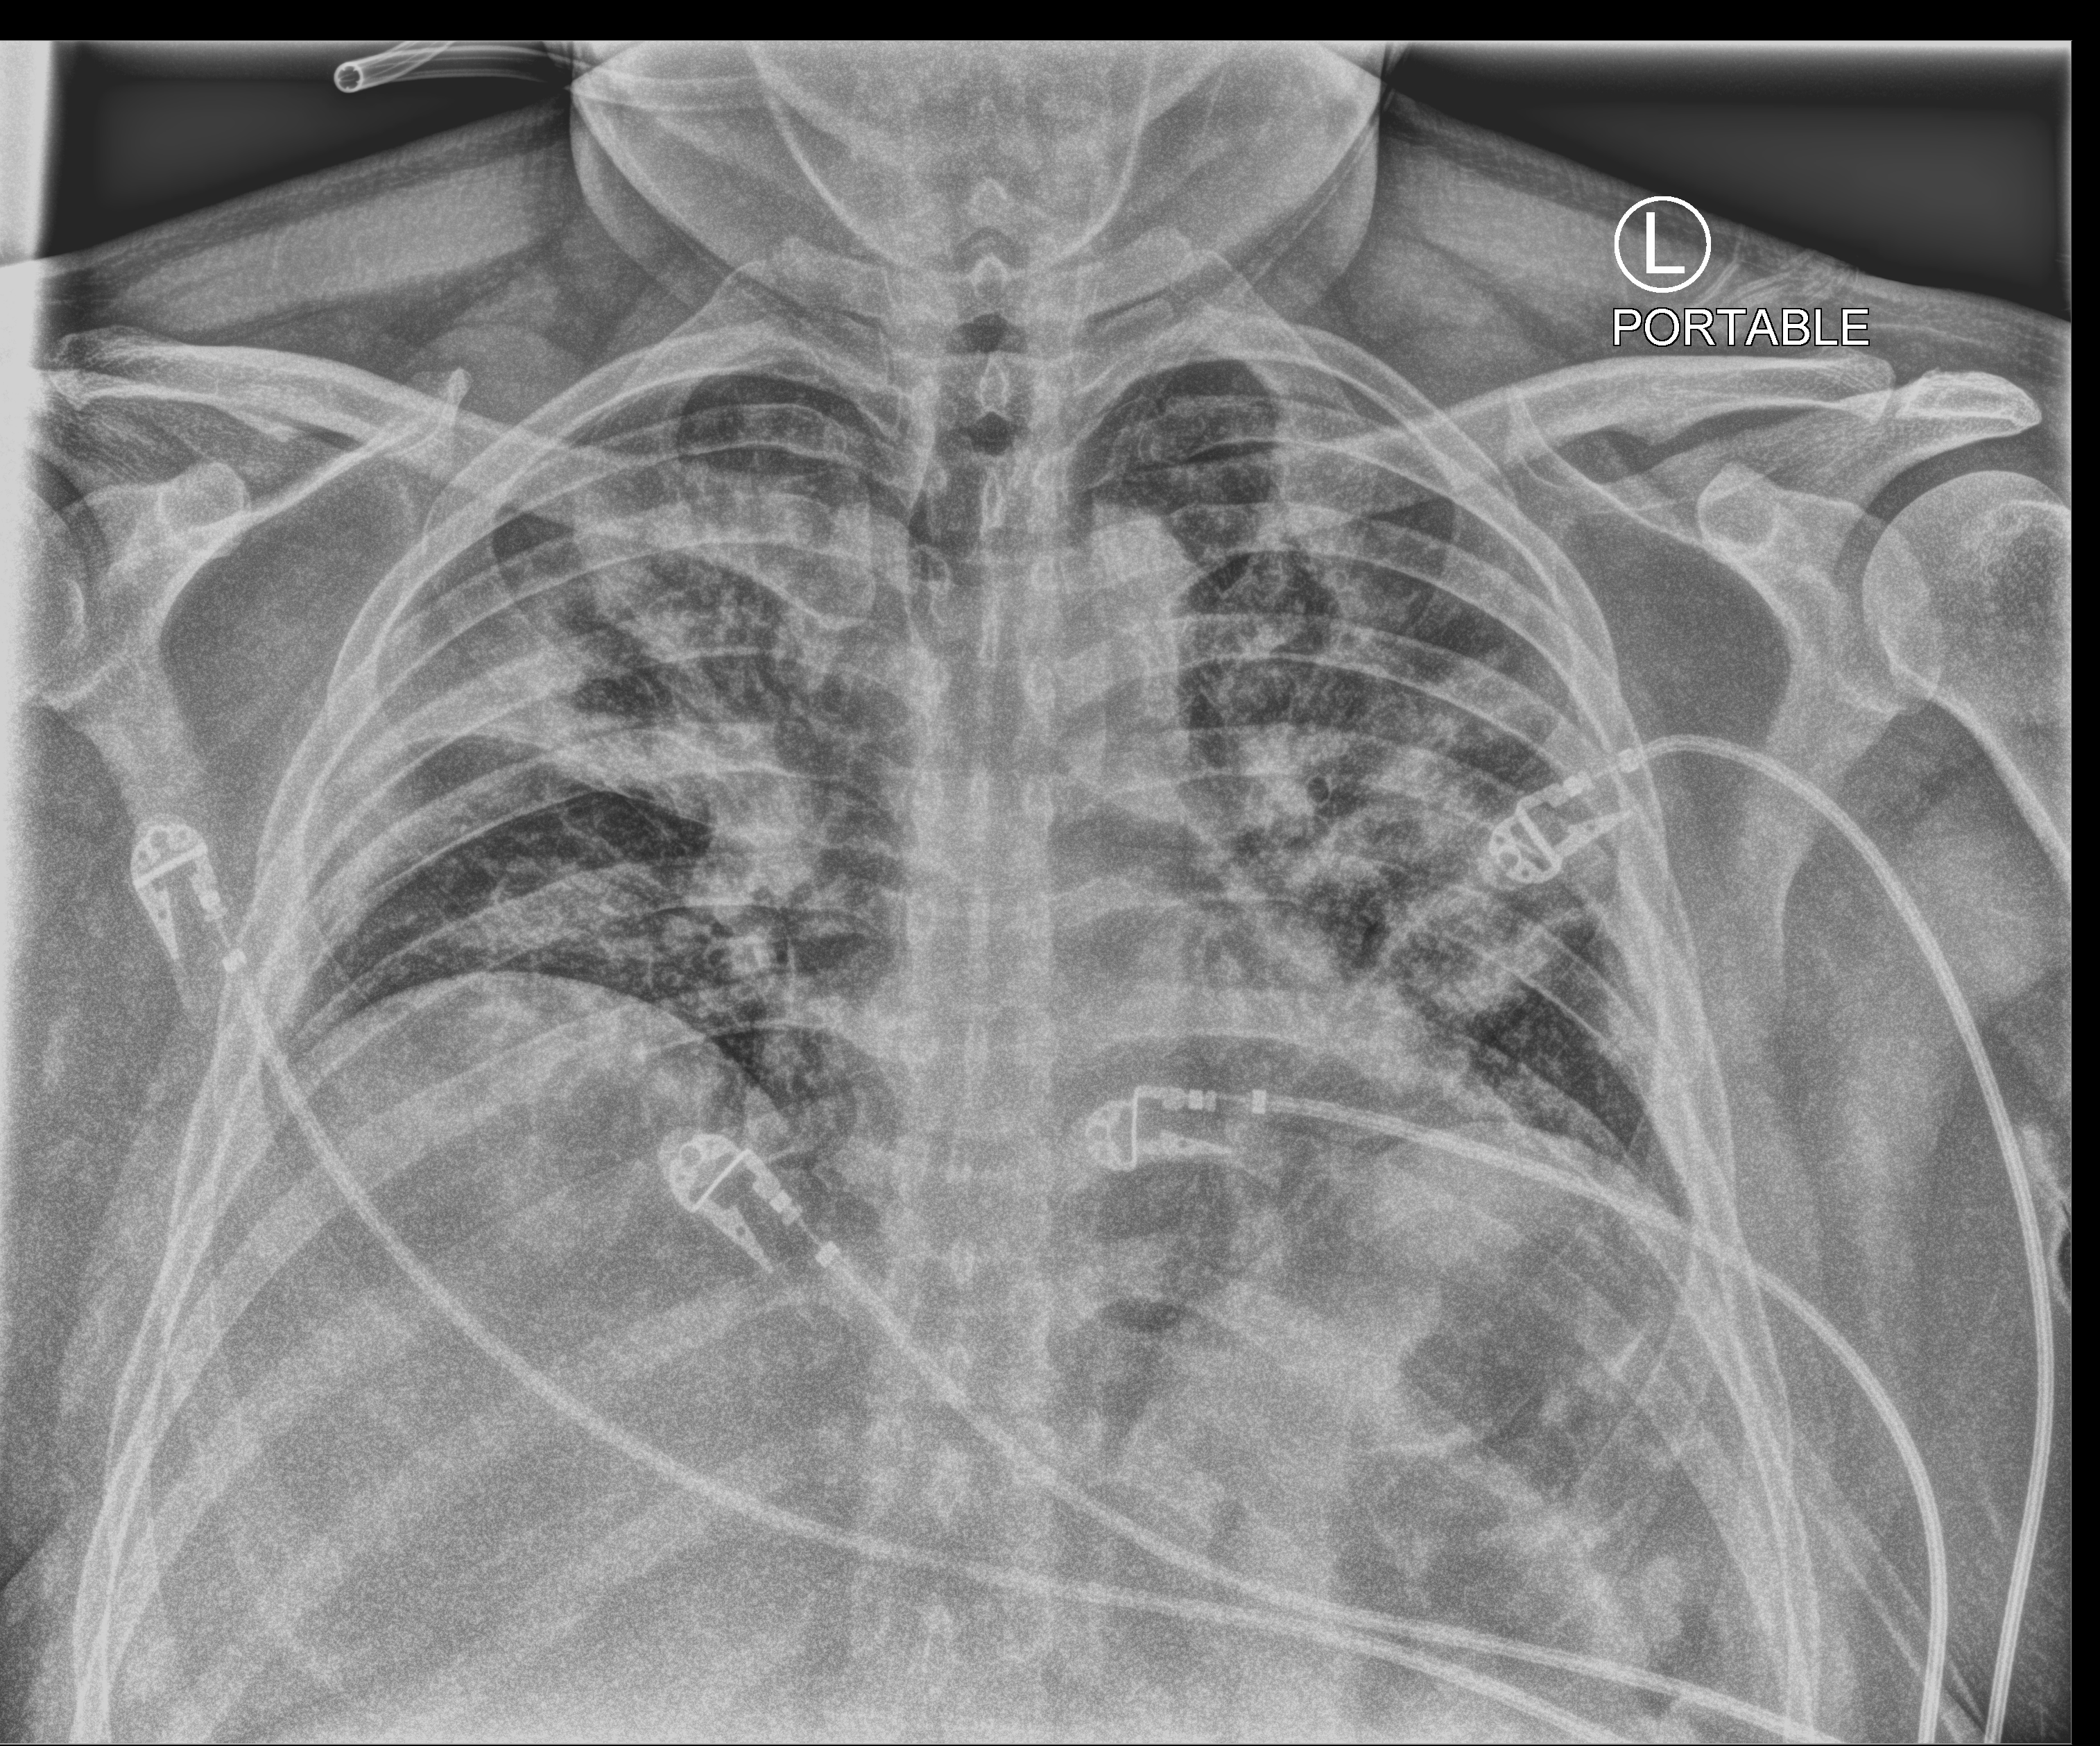
Portable chest radiograph; anteroposterior (AP) projection. Male patient hospitalised with COVID-19, age 18–59 years.
From the hospital-stay record, not from the radiograph (when in the stay this image was taken is not recorded):
- admitted to intensive care during this hospital stay: yes
- smoking status (admission record): never
- mechanically ventilated during this hospital stay: yes